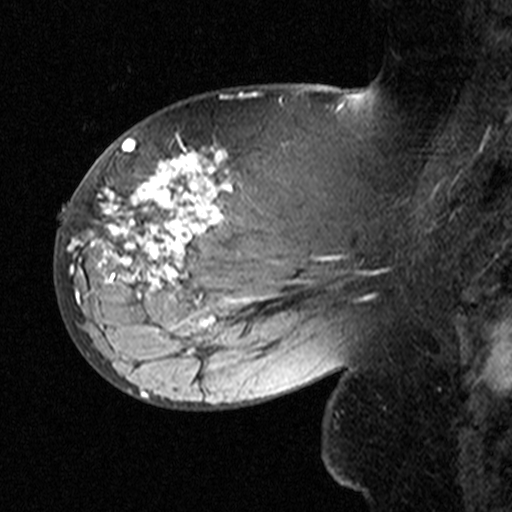
Breast MRI (dynamic contrast-enhanced), one sagittal slice; slice 21 of 44 in the series (ordered by position); dynamic contrast-enhanced study with each time point stored as its own series, time point 2 of 3 at this slice position (early post-contrast, ordered by acquisition time); 1.5 T; TE 4.5 ms, TR 11 ms; 3 mm slice thickness; 512 × 512 image matrix, field of view 200 × 200 mm. Patient: female, 53 years. Case-level facts recorded for this patient, not image findings: setting: breast cancer imaged before/during neoadjuvant chemotherapy; receptor status: HR-positive, HER2-negative.
Structures marked on this image (semi-automatically segmented with operator editing):
- analysis volume of interest (the breast-tissue region the enhancement analysis was run in; not a lesion): bounding box (x1, y1, x2, y2) in pixels: (76, 140, 311, 353)
- tumour enhancement mask (voxels above the 90 % enhancement threshold inside the analysis volume of interest): (76, 147, 232, 353)